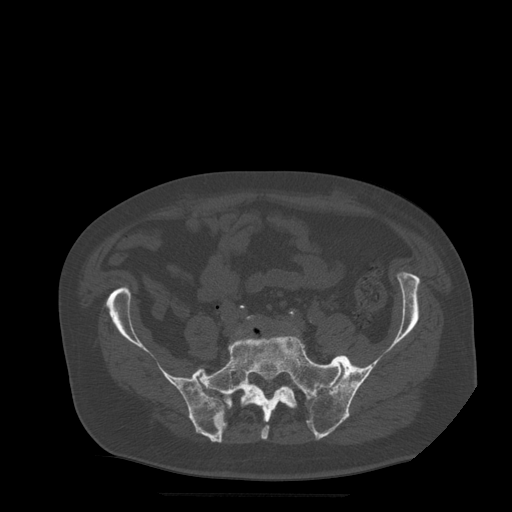
CT including the spine, one axial slice. Position 67 of 522 along the scan axis. Bone window (W 1800 / L 400 HU). 1.25 mm slice thickness. 512 × 512 image matrix. Patient age 72 years. From the clinical record (not read from this slice): primary cancer: prostate.
Annotated regions visible in this slice (semi-automatically segmented with operator editing):
- L5 vertebra: bounding box (x1, y1, x2, y2) in pixels: (246, 315, 255, 320)